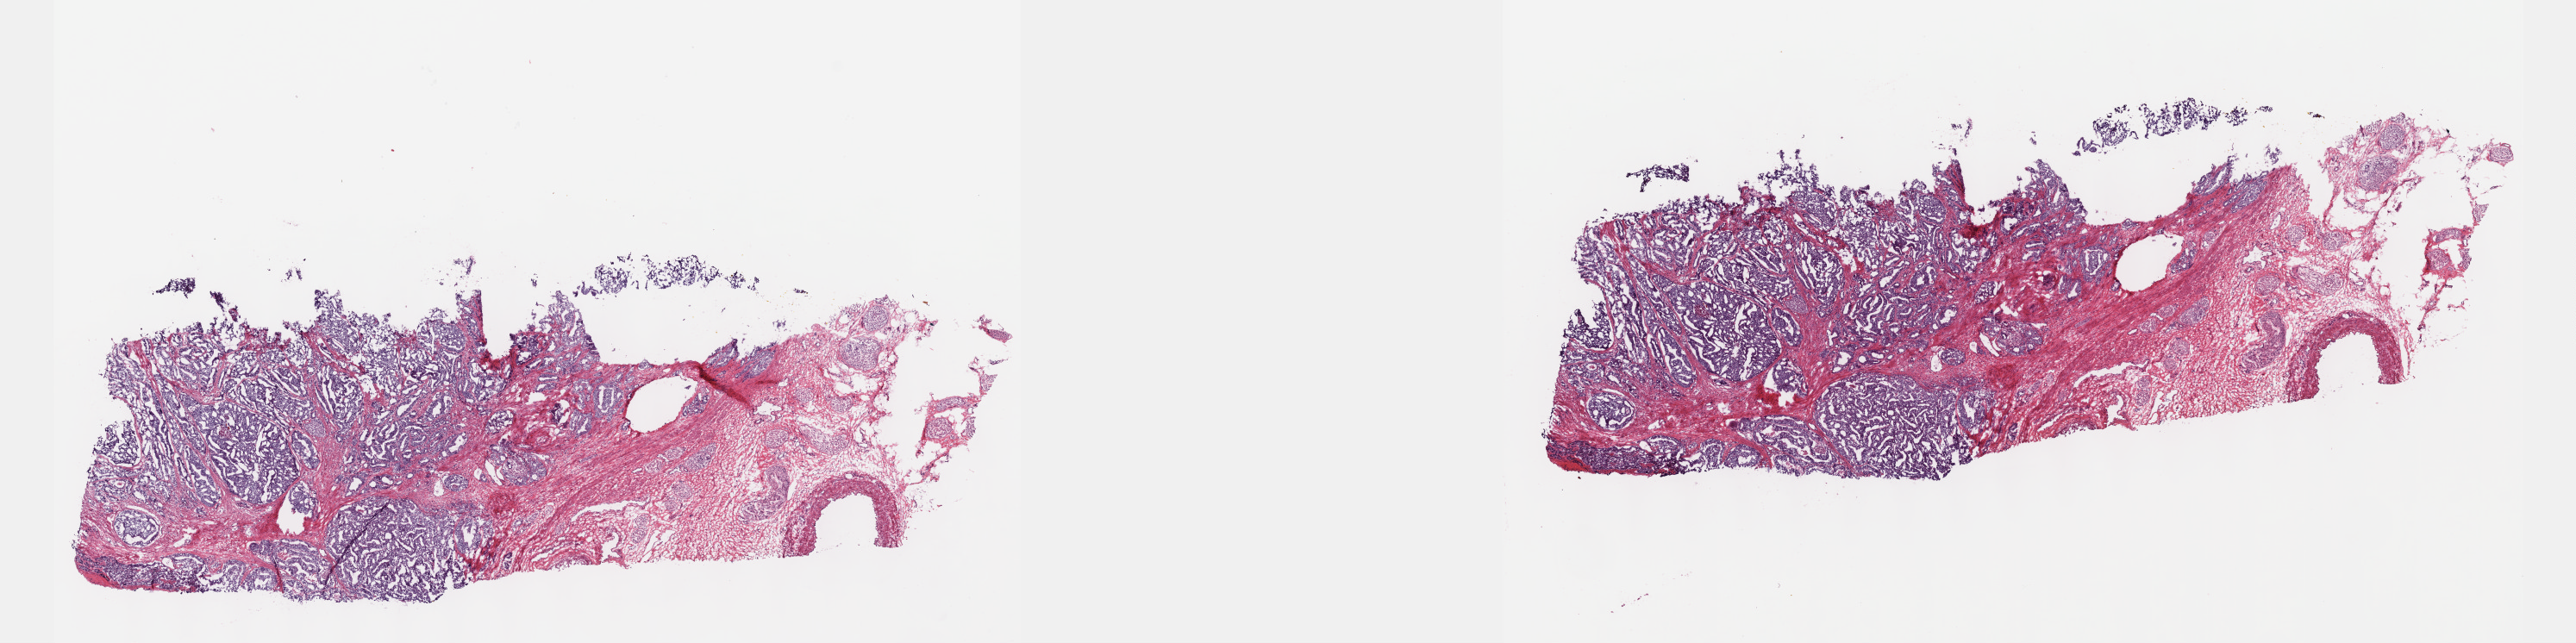
H&E-stained whole-slide image, shown as a low-resolution overview of the whole scanned area (about 24.1 x 6.0 mm, slide scanned at 40x); frozen section from the top of the tissue portion; primary tumour sample from the prostate. Male, age 54 years at initial diagnosis. Gleason score: 7 (4+3). Pathologist review of this section (percent, as recorded): tumour cells 75%, tumour nuclei 75%, normal cells 0%, stromal cells 25%, necrosis 0%. Inflammatory infiltration, as recorded: lymphocyte infiltration 2%, monocyte infiltration 0%, neutrophil infiltration 0%.
Pathologic diagnosis: Adenocarcinoma, NOS (prostate gland). Laterality: right. Lymph nodes positive (case pathology): 0 of 16 examined.